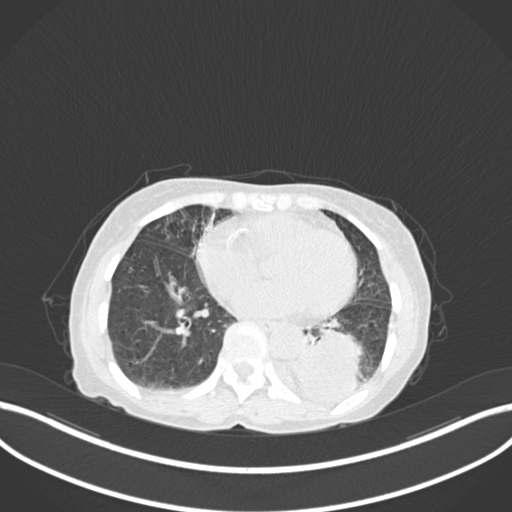
Chest CT, one axial slice. Position 45 of 233 along the scan axis. 120 kVp. Lung window (W 1500 / L -600 HU). 1 mm slice thickness. 512 × 512 image matrix. Female patient, age 78 years. From the clinical record (not read from this slice): clinical TNM (as recorded): T3 N0 M1.
Outlined on this slice (rectangle marked by the reading radiologist):
- lung tumour (recorded histology: squamous cell carcinoma): bounding box <293,322,372,405> (left, top, right, bottom; pixels)